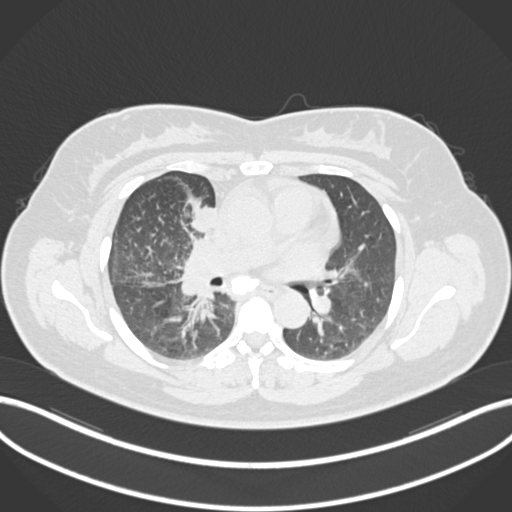
Chest CT, one axial slice; position 95 of 183 along the scan axis; reconstruction kernel B30f; 120 kVp; lung window (W 1500 / L -600 HU); 512 × 512 image matrix, field of view 400 × 400 mm. Female patient, age 46 years. From the clinical record (not read from this slice): clinical TNM (as recorded): T2a N1 M0.
Structures marked on this image (rectangle marked by the reading radiologist):
- lung tumour (recorded histology: adenocarcinoma): box from (x=187, y=201) to (x=222, y=238) px